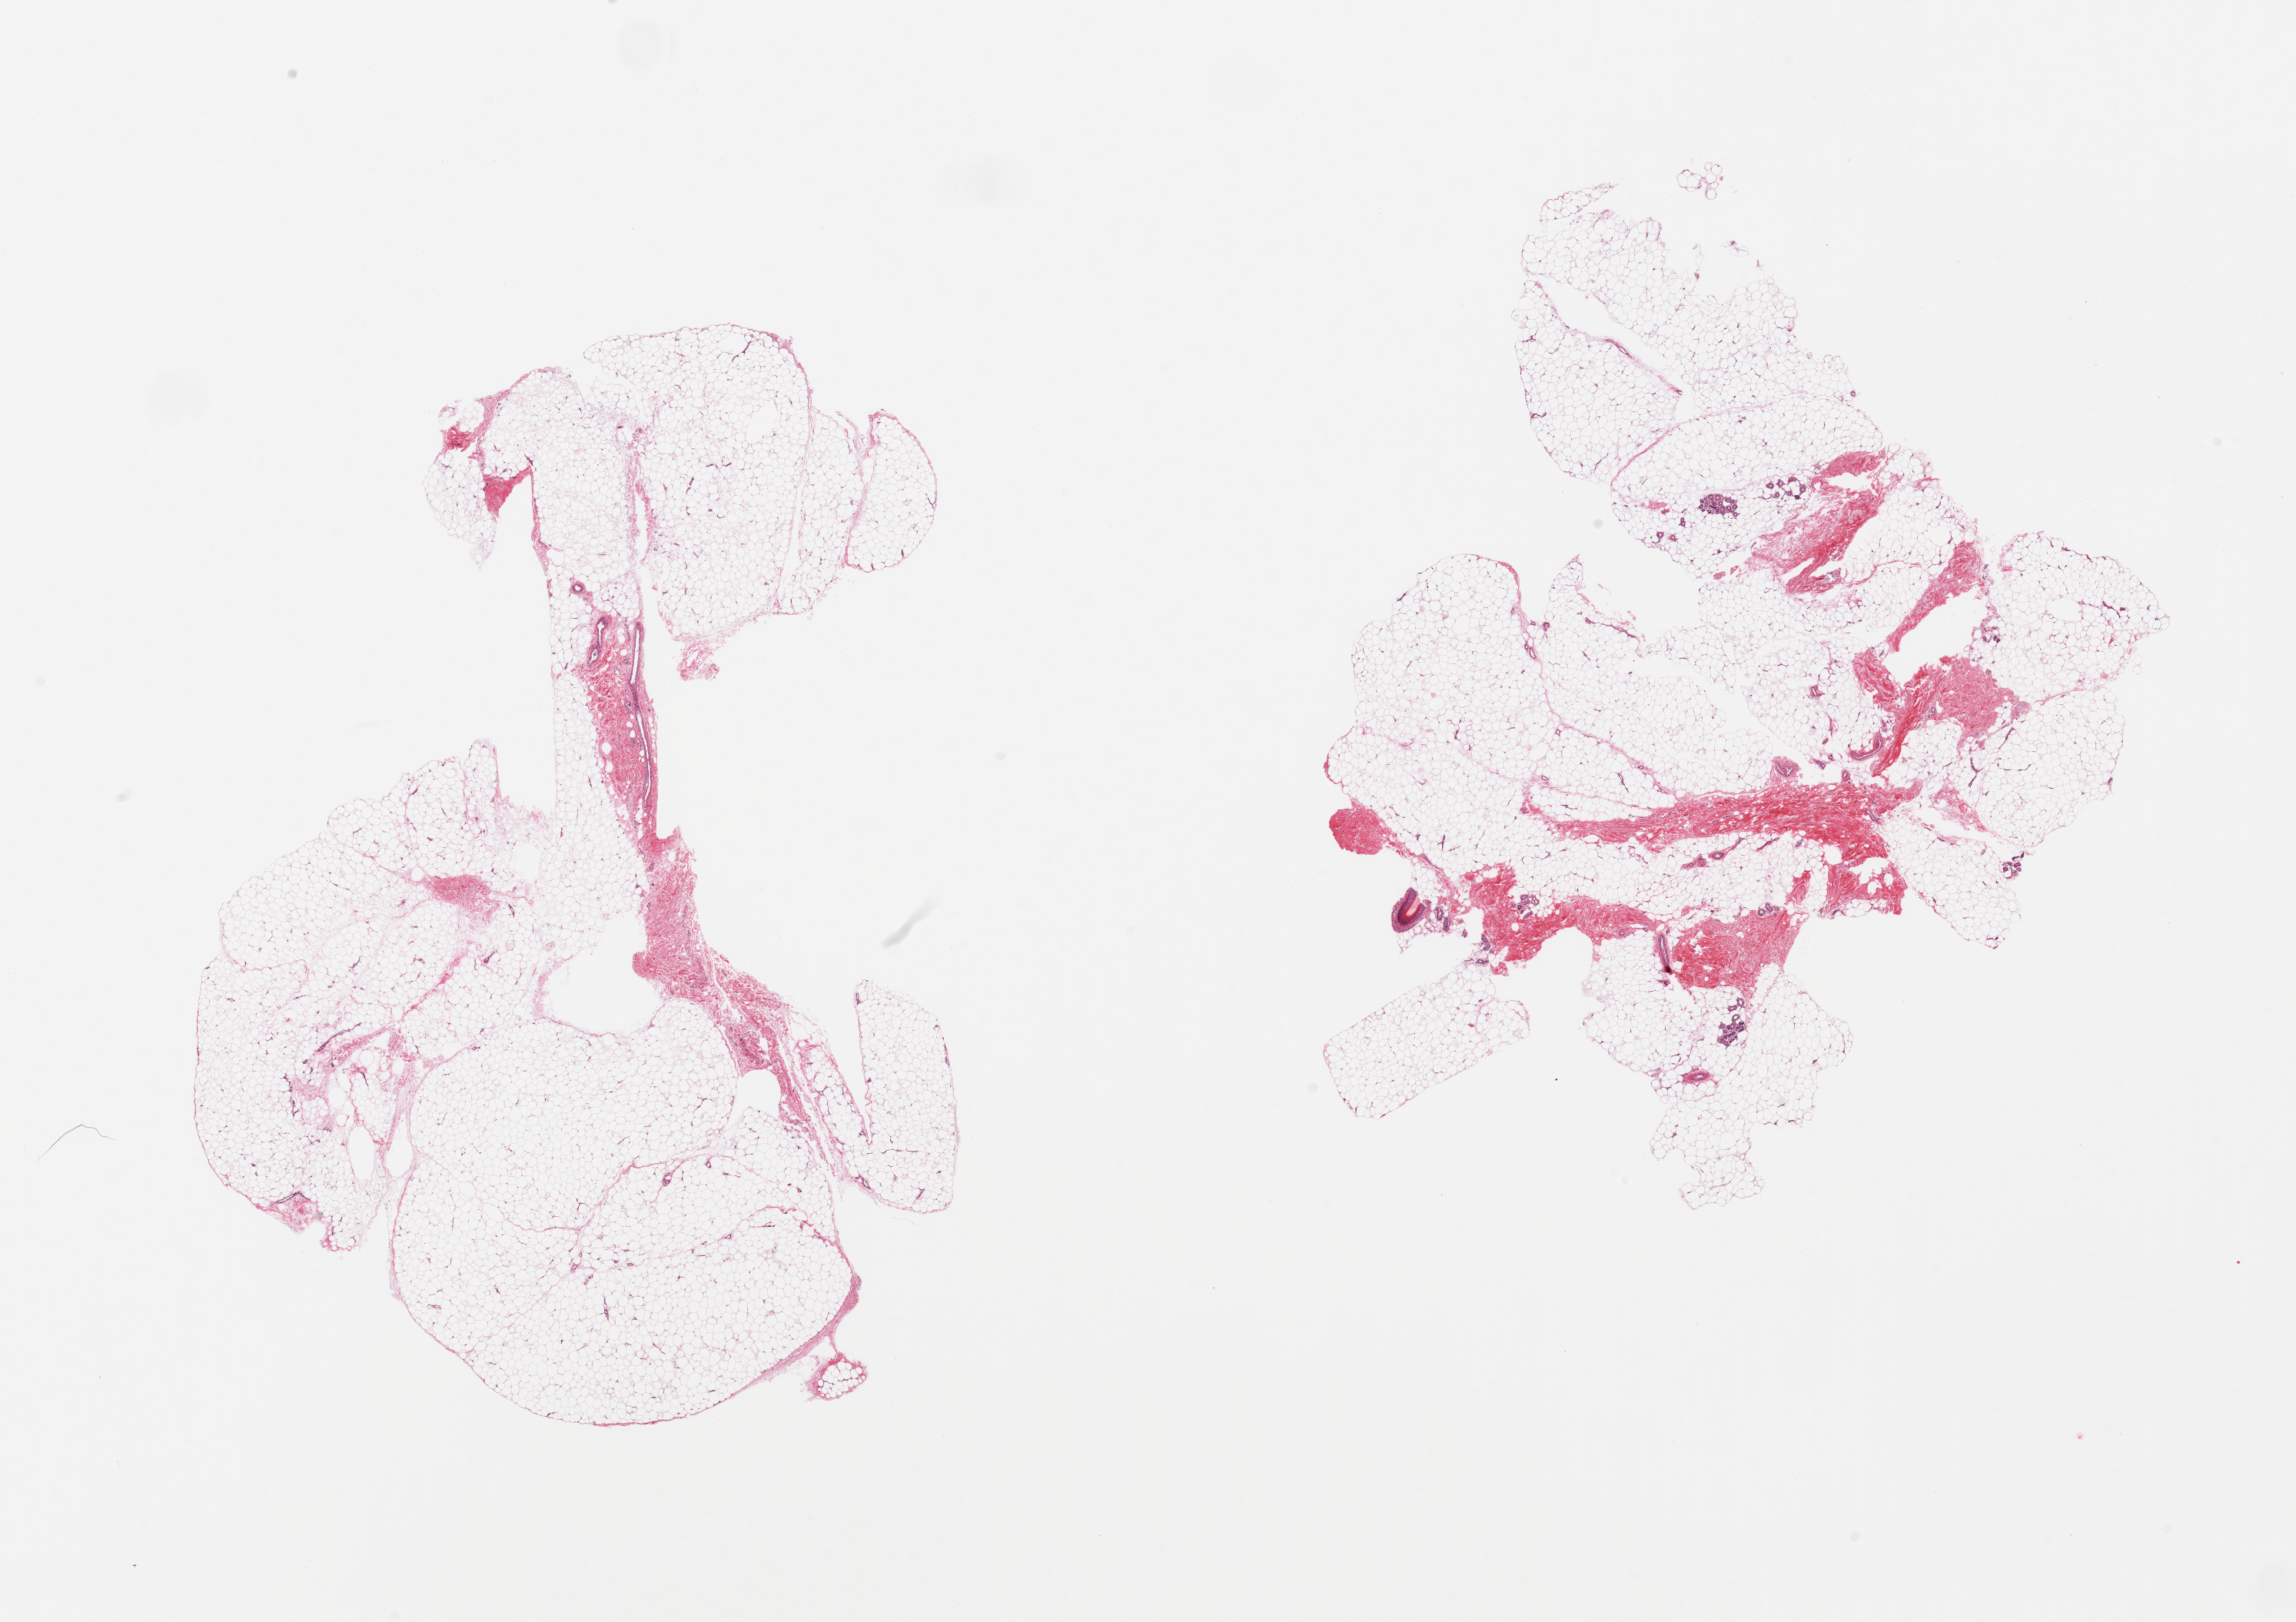
Digitized hematoxylin and eosin (H&E)-stained section, brightfield — whole scanned area (about 23.6 x 16.7 mm) shown as a low-resolution overview; PAXgene-fixed, paraffin-embedded tissue; section of adipose tissue (target tissue); donor tissue sample. Male donor.
Review note (as recorded): 2 pieces; predominantly fat with ~10% fibrous tissue, scattered sweat glands and portion of hair follicle.